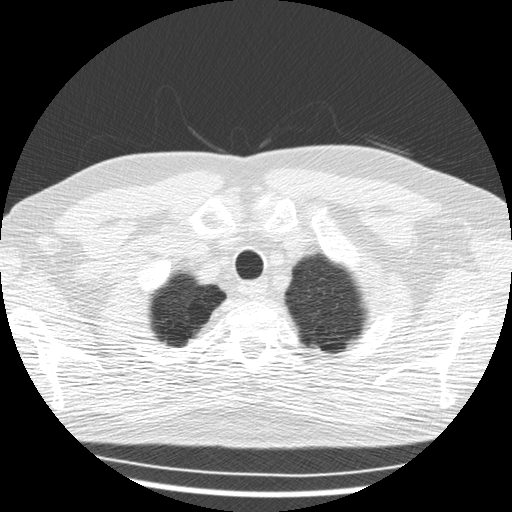
Low-dose screening chest CT, axial slice. First (baseline) screen. Lung window (W 1500 / L -600 HU). 2.5 mm slice thickness. Slice 28 of 168 in the series. Male participant, aged 57 years at enrolment. Former smoker at enrolment.
• Lesion marked by an expert reader, bounding box (x1, y1, x2, y2) in pixels: (304, 329, 333, 355).
• Screening reader's record for this exam (one nodule recorded; not confirmed to be the boxed lesion): non-calcified nodule or mass ≥4 mm, right upper lobe, 7 × 6 mm, smooth margins, soft tissue attenuation.
• Note: the box lies in the patient's left hemithorax on this image, whereas the reader's record names the right lung; they may be different findings.